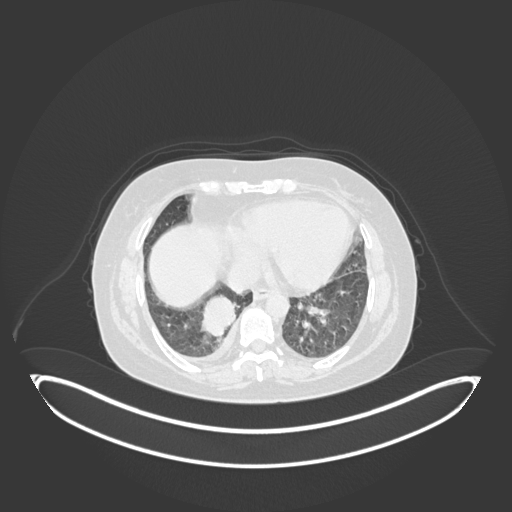
Chest CT, one axial slice; position 45 of 231 along the scan axis; 120 kVp; lung window (W 1500 / L -600 HU); 1 mm slice thickness; 512 × 512 image matrix, field of view 500 × 500 mm. Female patient, age 56 years. Case-level facts recorded for this patient, not image findings: clinical TNM (as recorded): T2b N1 M0.
Annotated regions visible in this slice (rectangle marked by the reading radiologist):
- lung tumour (recorded histology: small cell carcinoma): bounding box <199,292,244,344> (left, top, right, bottom; pixels)